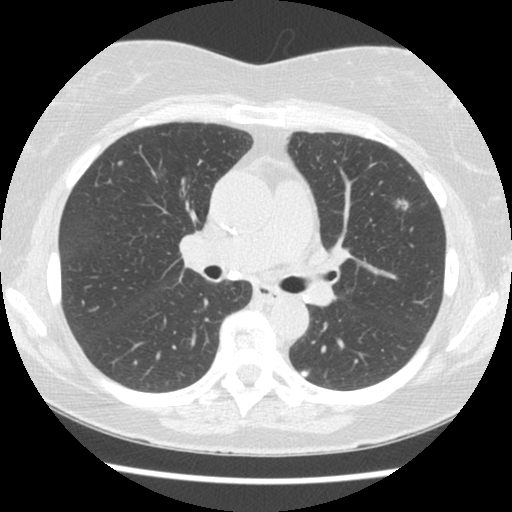
Low-dose screening chest CT, axial slice, second screening round (one year after baseline), lung window (W 1500 / L -600 HU), slice 51 of 120 in the series. Female participant, aged 60 years at enrolment.
Expert reader's lesion annotation, bounding box <377,191,421,226> (left, top, right, bottom; pixels). The screening reader recorded 3 non-calcified nodules or masses ≥4 mm on this exam (left upper lobe, left upper lobe, right upper lobe); which of them this box marks is not recorded. Official screen result: positive, other. Later outcome: lung cancer diagnosed 62 days after this screen — non-small cell carcinoma, left upper lobe, poorly differentiated (G3), stage IA (AJCC 6th edition), 10 mm at pathology.